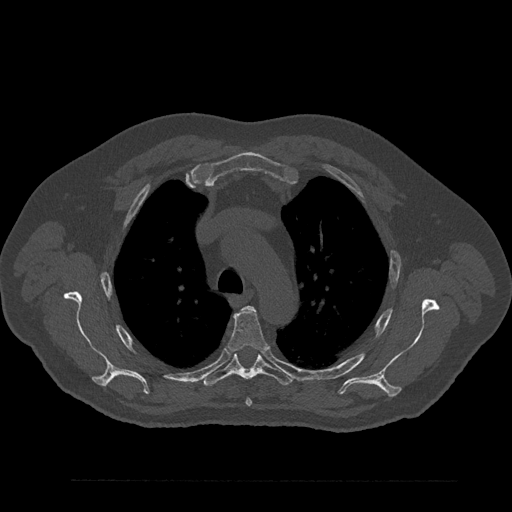
CT including the spine, one axial slice; slice 625 of 797 in the series (ordered by position); 120 kVp; bone window (W 1800 / L 400 HU); 0.5 mm slice thickness; 512 × 512 image matrix, field of view 430 × 430 mm. Patient: male, 61 years. Case-level facts recorded for this patient, not image findings: primary cancer: prostate.
Annotated regions visible in this slice (semi-automatic segmentation, software-assisted and operator-edited):
- T4 vertebra: box from (x=228, y=307) to (x=268, y=406) px
- T5 vertebra: (x=202, y=353)–(x=292, y=387)